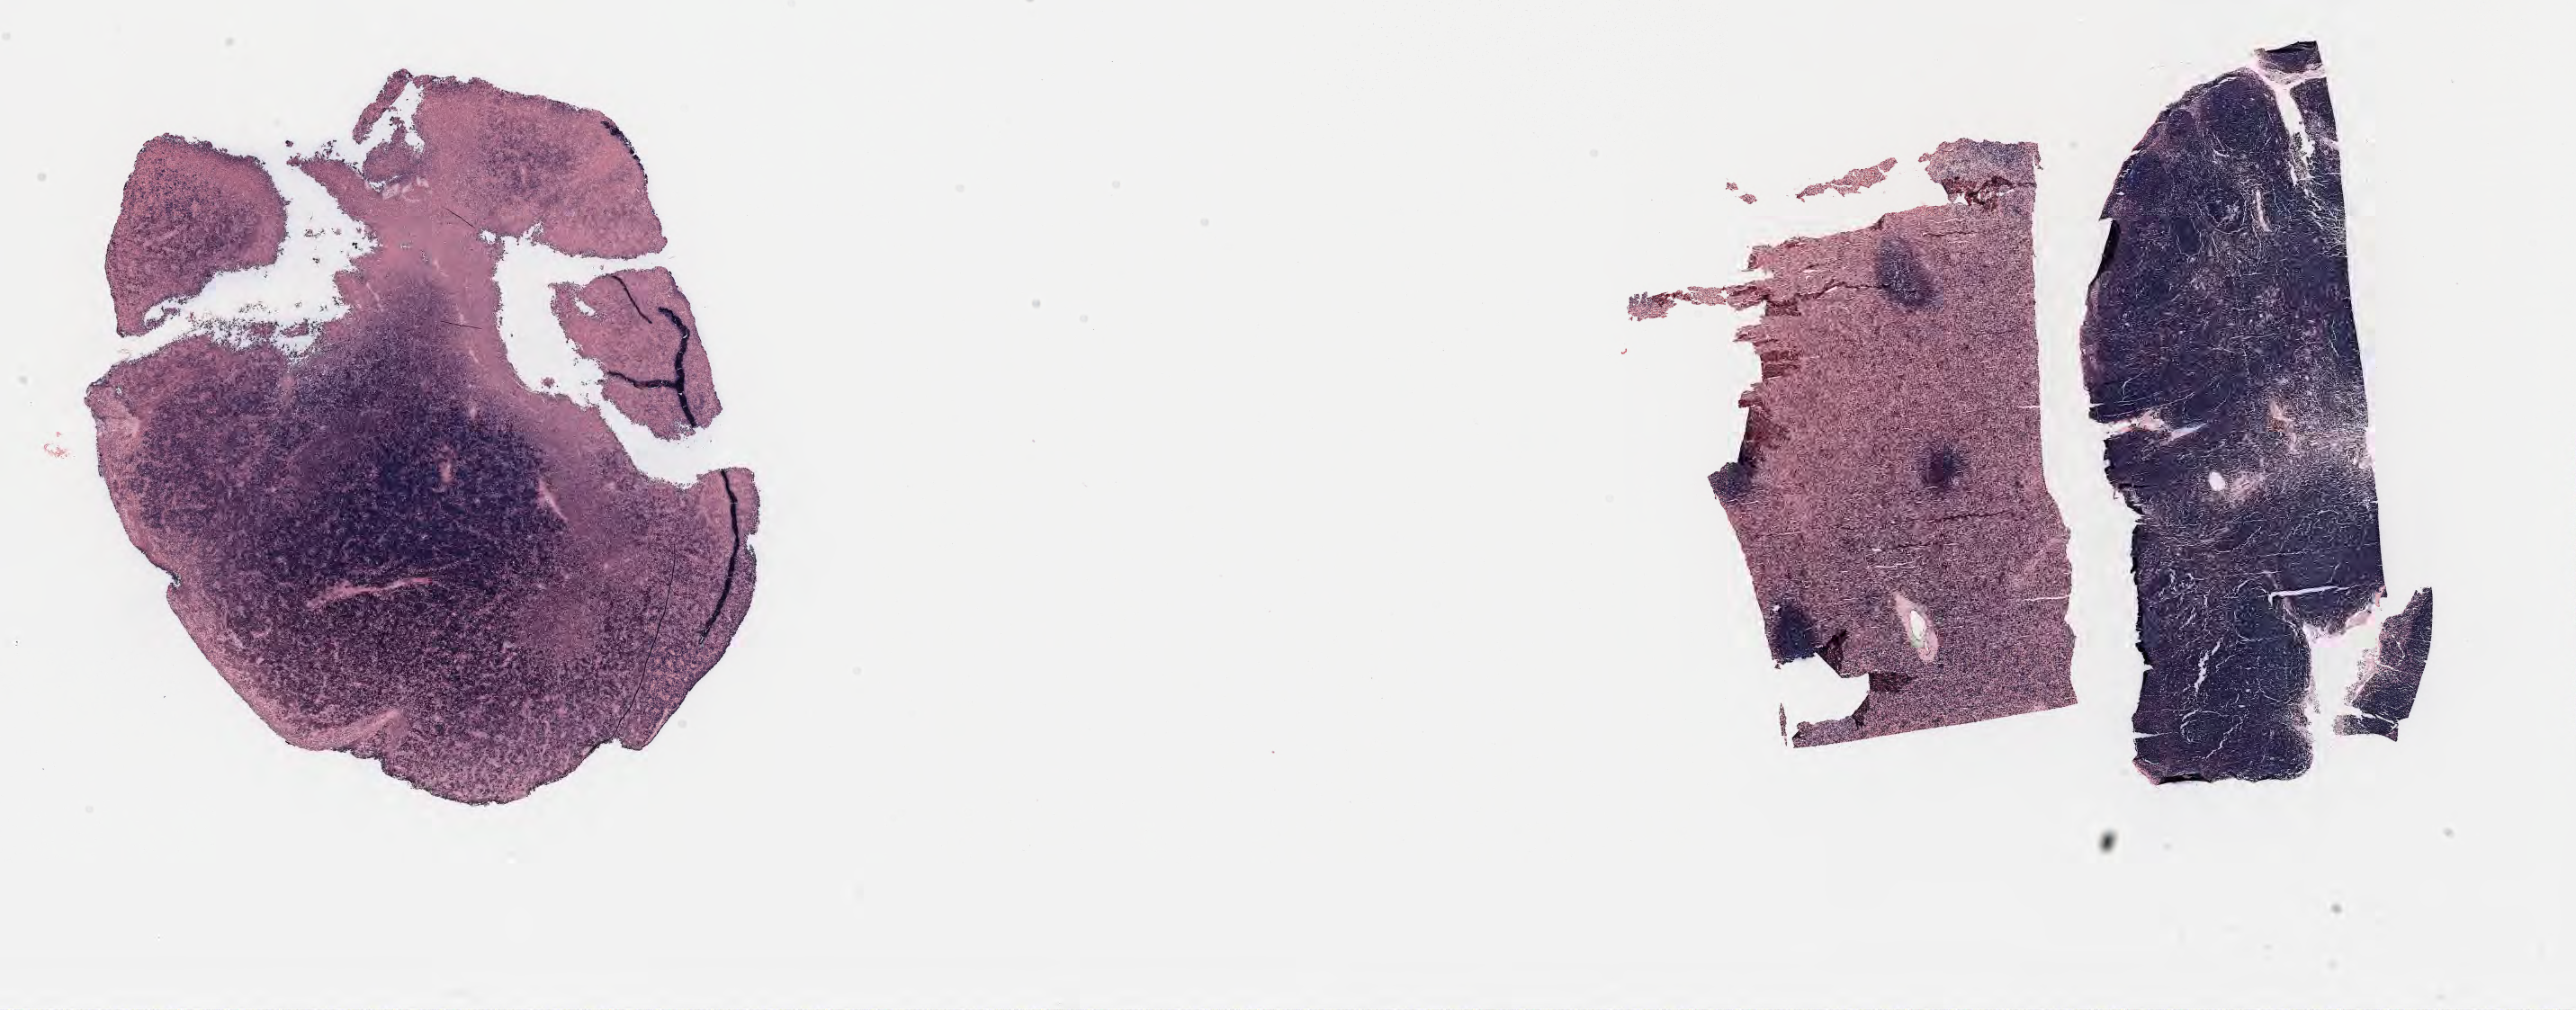
Whole-slide image; stain recorded as Iodonitrotetrazolium, a low-resolution overview of the entire scanned area, about 23.2 x 9.1 mm. Specimen: tumor tissue. Anatomic site: liver. Male patient, 46 years old.
Diagnosis: Diffuse large B-cell lymphoma, NOS.